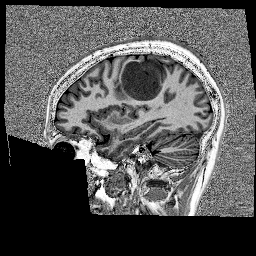
Brain MRI from a brain-tumour surgery series, one sagittal slice; slice 57 of 176 in the series (ordered by position); 1 mm slice thickness; 256 × 256 image matrix, field of view 256 × 256 mm. Case-level facts recorded for this patient, not image findings: histopathology: Glioblastoma; WHO grade: 4; IDH mutation: no; tumour location: Left Frontal.
Annotated regions visible in this slice (manually delineated by an expert):
- tumour: bounding box (x1, y1, x2, y2) in pixels: (118, 58, 175, 105)